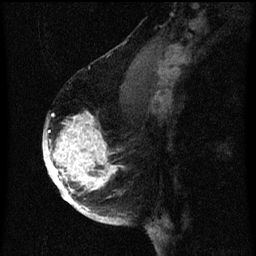
Breast MRI (dynamic contrast-enhanced), one sagittal slice. Slice 42 of 60 in the series (ordered by position). Dynamic contrast-enhanced series, image 2 of 3 at this slice position (ordered by acquisition). 1.5 T. TE 4.2 ms, TR 8 ms. 256 × 256 image matrix, field of view 180 × 180 mm. Female patient, age 56 years.
Outlined on this slice (semi-automatically segmented with operator editing):
- analysis volume of interest (the breast-tissue region the enhancement analysis was run in; not a lesion): bounding box [x1, y1, x2, y2] px = [44, 114, 121, 219]
- tumour enhancement mask (voxels above the 70 % enhancement threshold inside the analysis volume of interest): [44, 116, 119, 219]